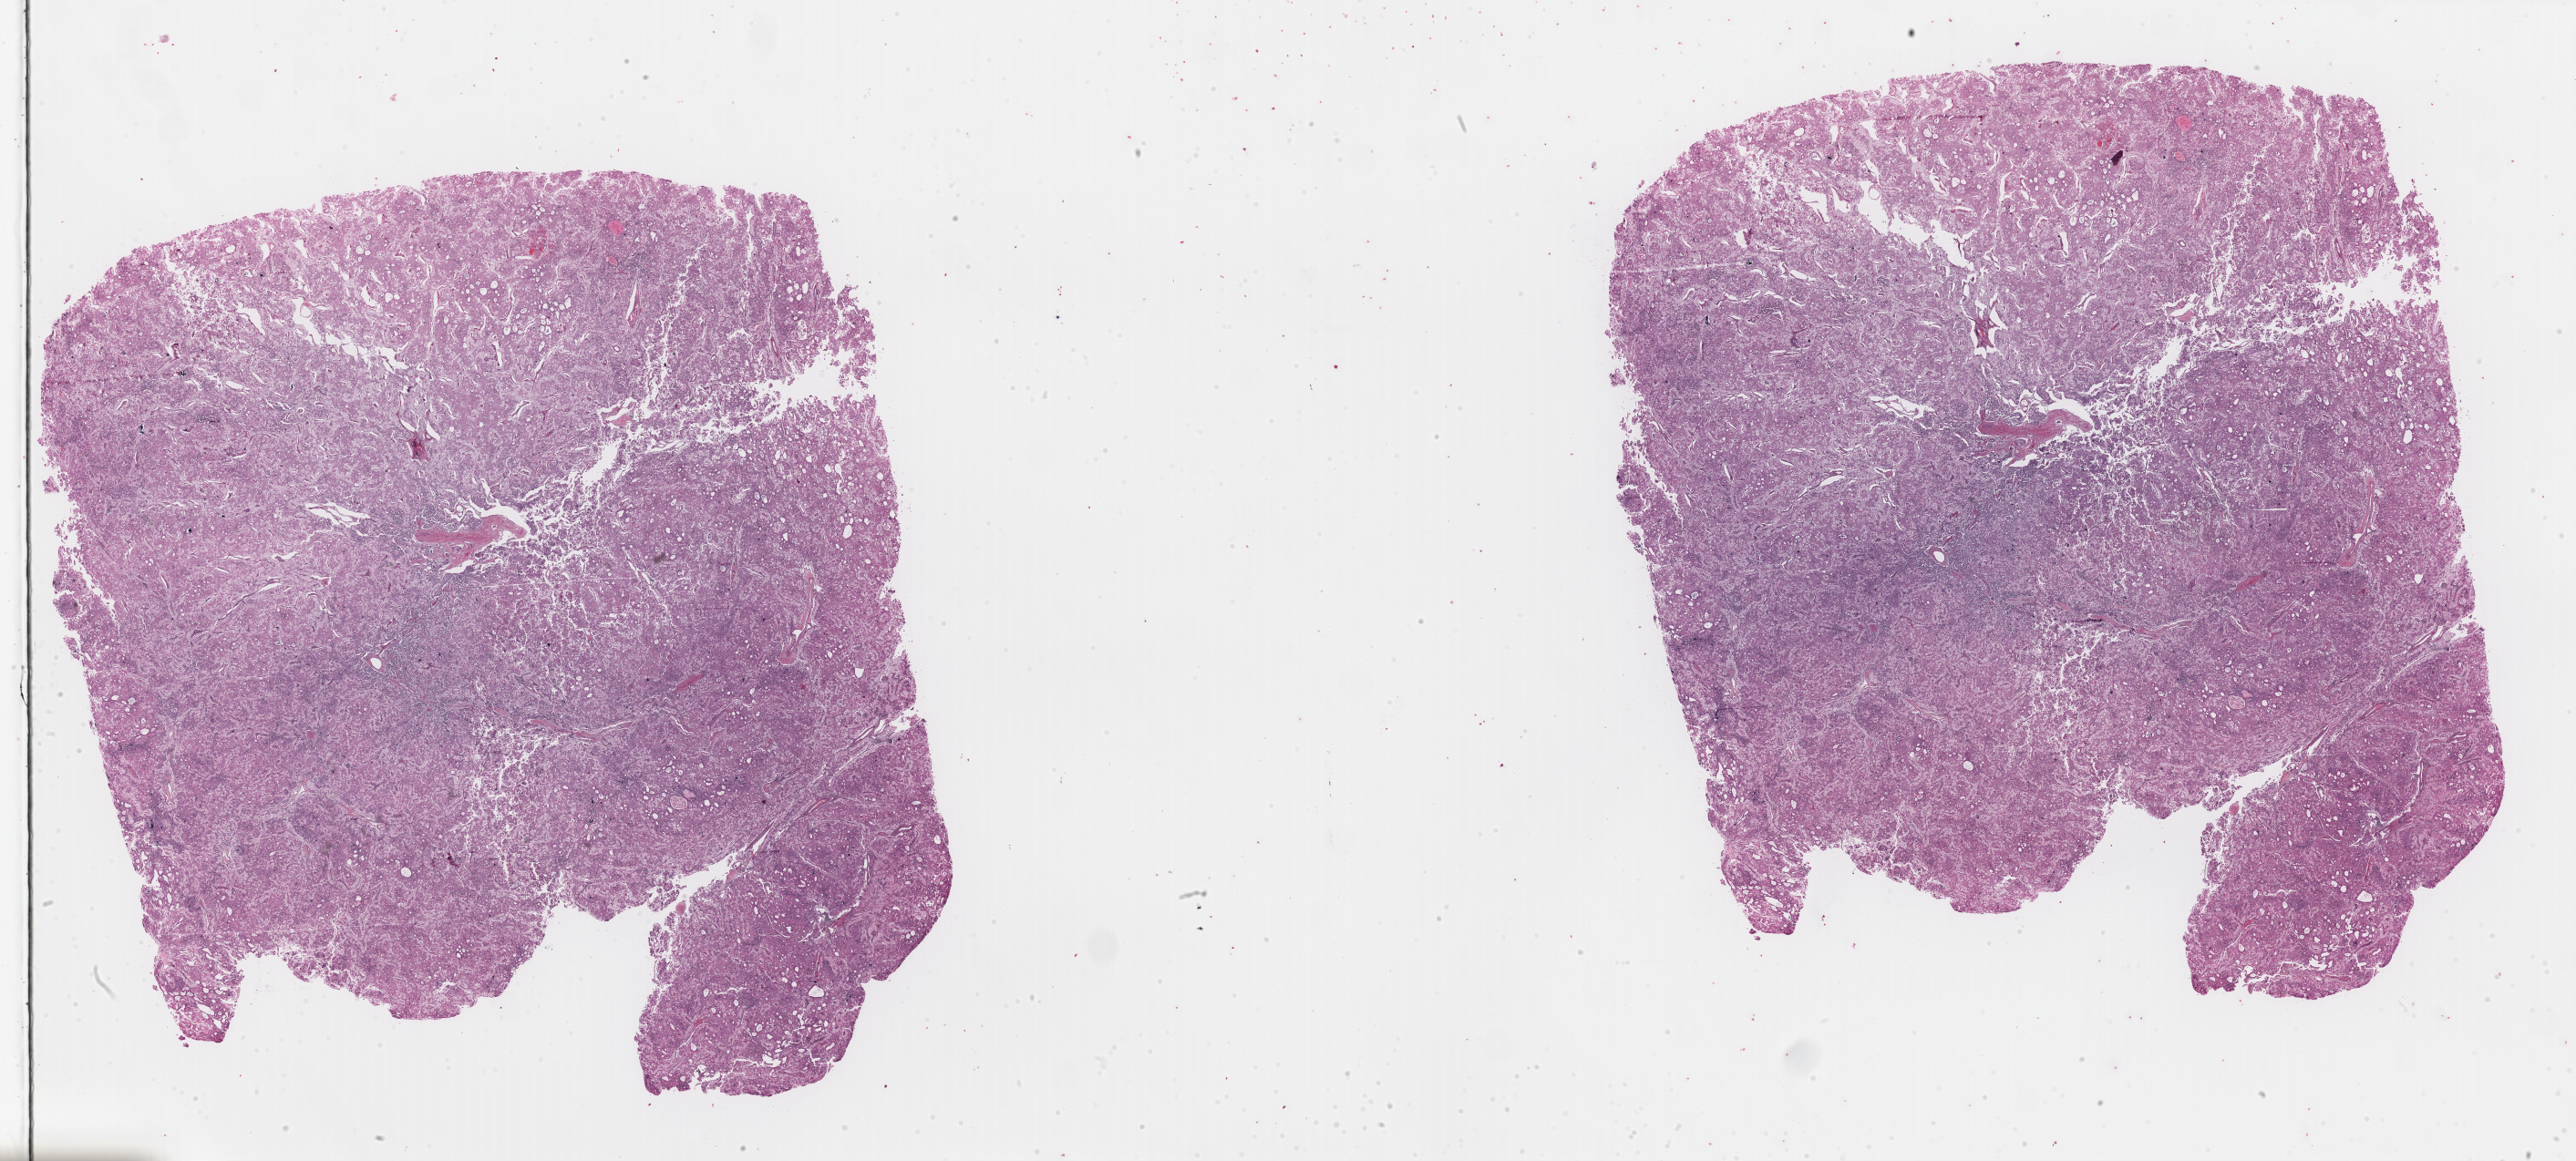
Whole-slide histology image, Hematoxylin and eosin (H&E) stained, a low-resolution overview of the entire scanned area, about 44.7 x 20.2 mm, formalin-fixed paraffin-embedded (FFPE) diagnostic section, sample: primary tumour, kidney. Patient: female, age at initial diagnosis 61 years.
- AJCC pathologic stage: I (7th edition)
- pathologic diagnosis: Renal cell carcinoma, chromophobe type
- laterality: right